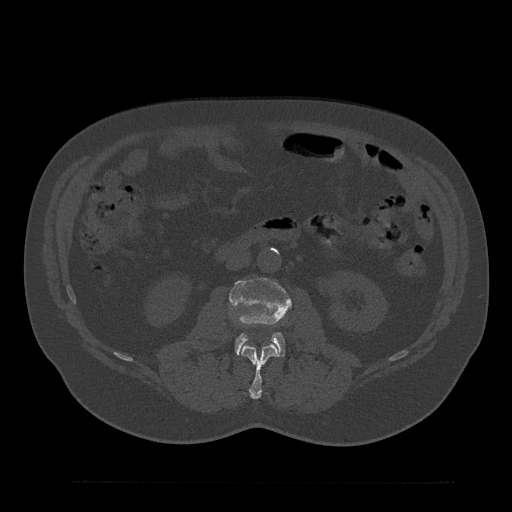
CT including the spine, one axial slice; slice 66 of 797 in the series (ordered by position); reconstruction kernel Br40s/3; bone window (W 1800 / L 400 HU); 0.5 mm slice thickness; 512 × 512 image matrix, field of view 430 × 430 mm. Patient: male, 61 years. Case-level facts recorded for this patient, not image findings: primary cancer: prostate.
Structures marked on this image (semi-automatically segmented with operator editing):
- L2 vertebra: box from (x=241, y=344) to (x=279, y=399) px
- L3 vertebra: (x=231, y=277)–(x=292, y=357)